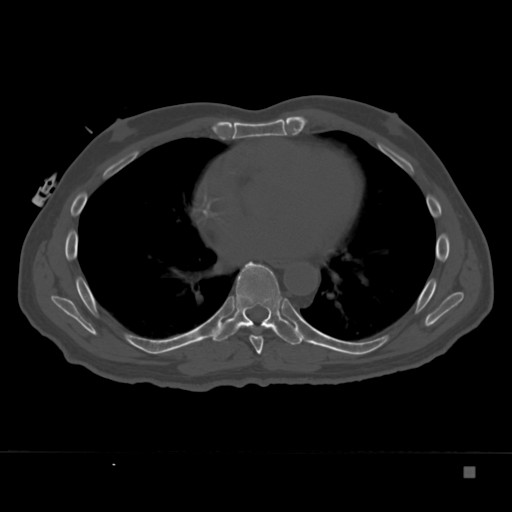
CT including the spine, one axial slice. Slice 213 of 332 in the series (ordered by position). Reconstruction kernel Br40s. Bone window (W 1800 / L 400 HU). 1.5 mm slice thickness. 512 × 512 image matrix. Male patient, age 72 years. Case-level facts recorded for this patient, not image findings: primary cancer: skeletal.
Annotated regions visible in this slice (semi-automatic segmentation, software-assisted and operator-edited):
- T7 vertebra: bounding box (x1, y1, x2, y2) in pixels: (249, 335, 264, 355)
- T8 vertebra: (211, 261, 307, 345)